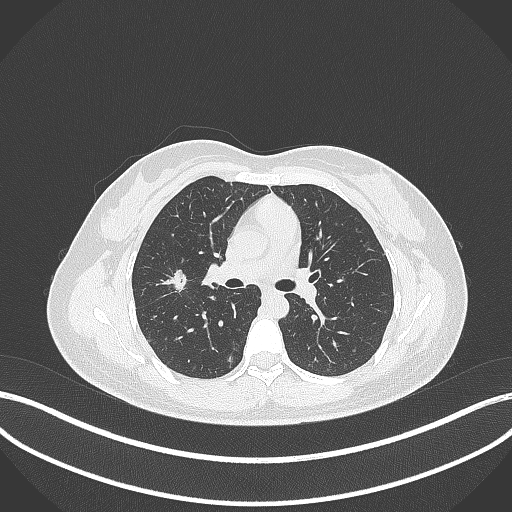
Chest CT, one axial slice. Position 198 of 307 along the scan axis. Lung window (W 1500 / L -600 HU). 512 × 512 image matrix, field of view 400 × 400 mm. Patient: female, 33 years. Case-level facts recorded for this patient, not image findings: clinical TNM (as recorded): T1c N0 M0; histopathological grade: G2-G3.
Outlined on this slice (rectangle marked by the reading radiologist):
- lung tumour (recorded histology: adenocarcinoma): box from (x=158, y=264) to (x=191, y=294) px